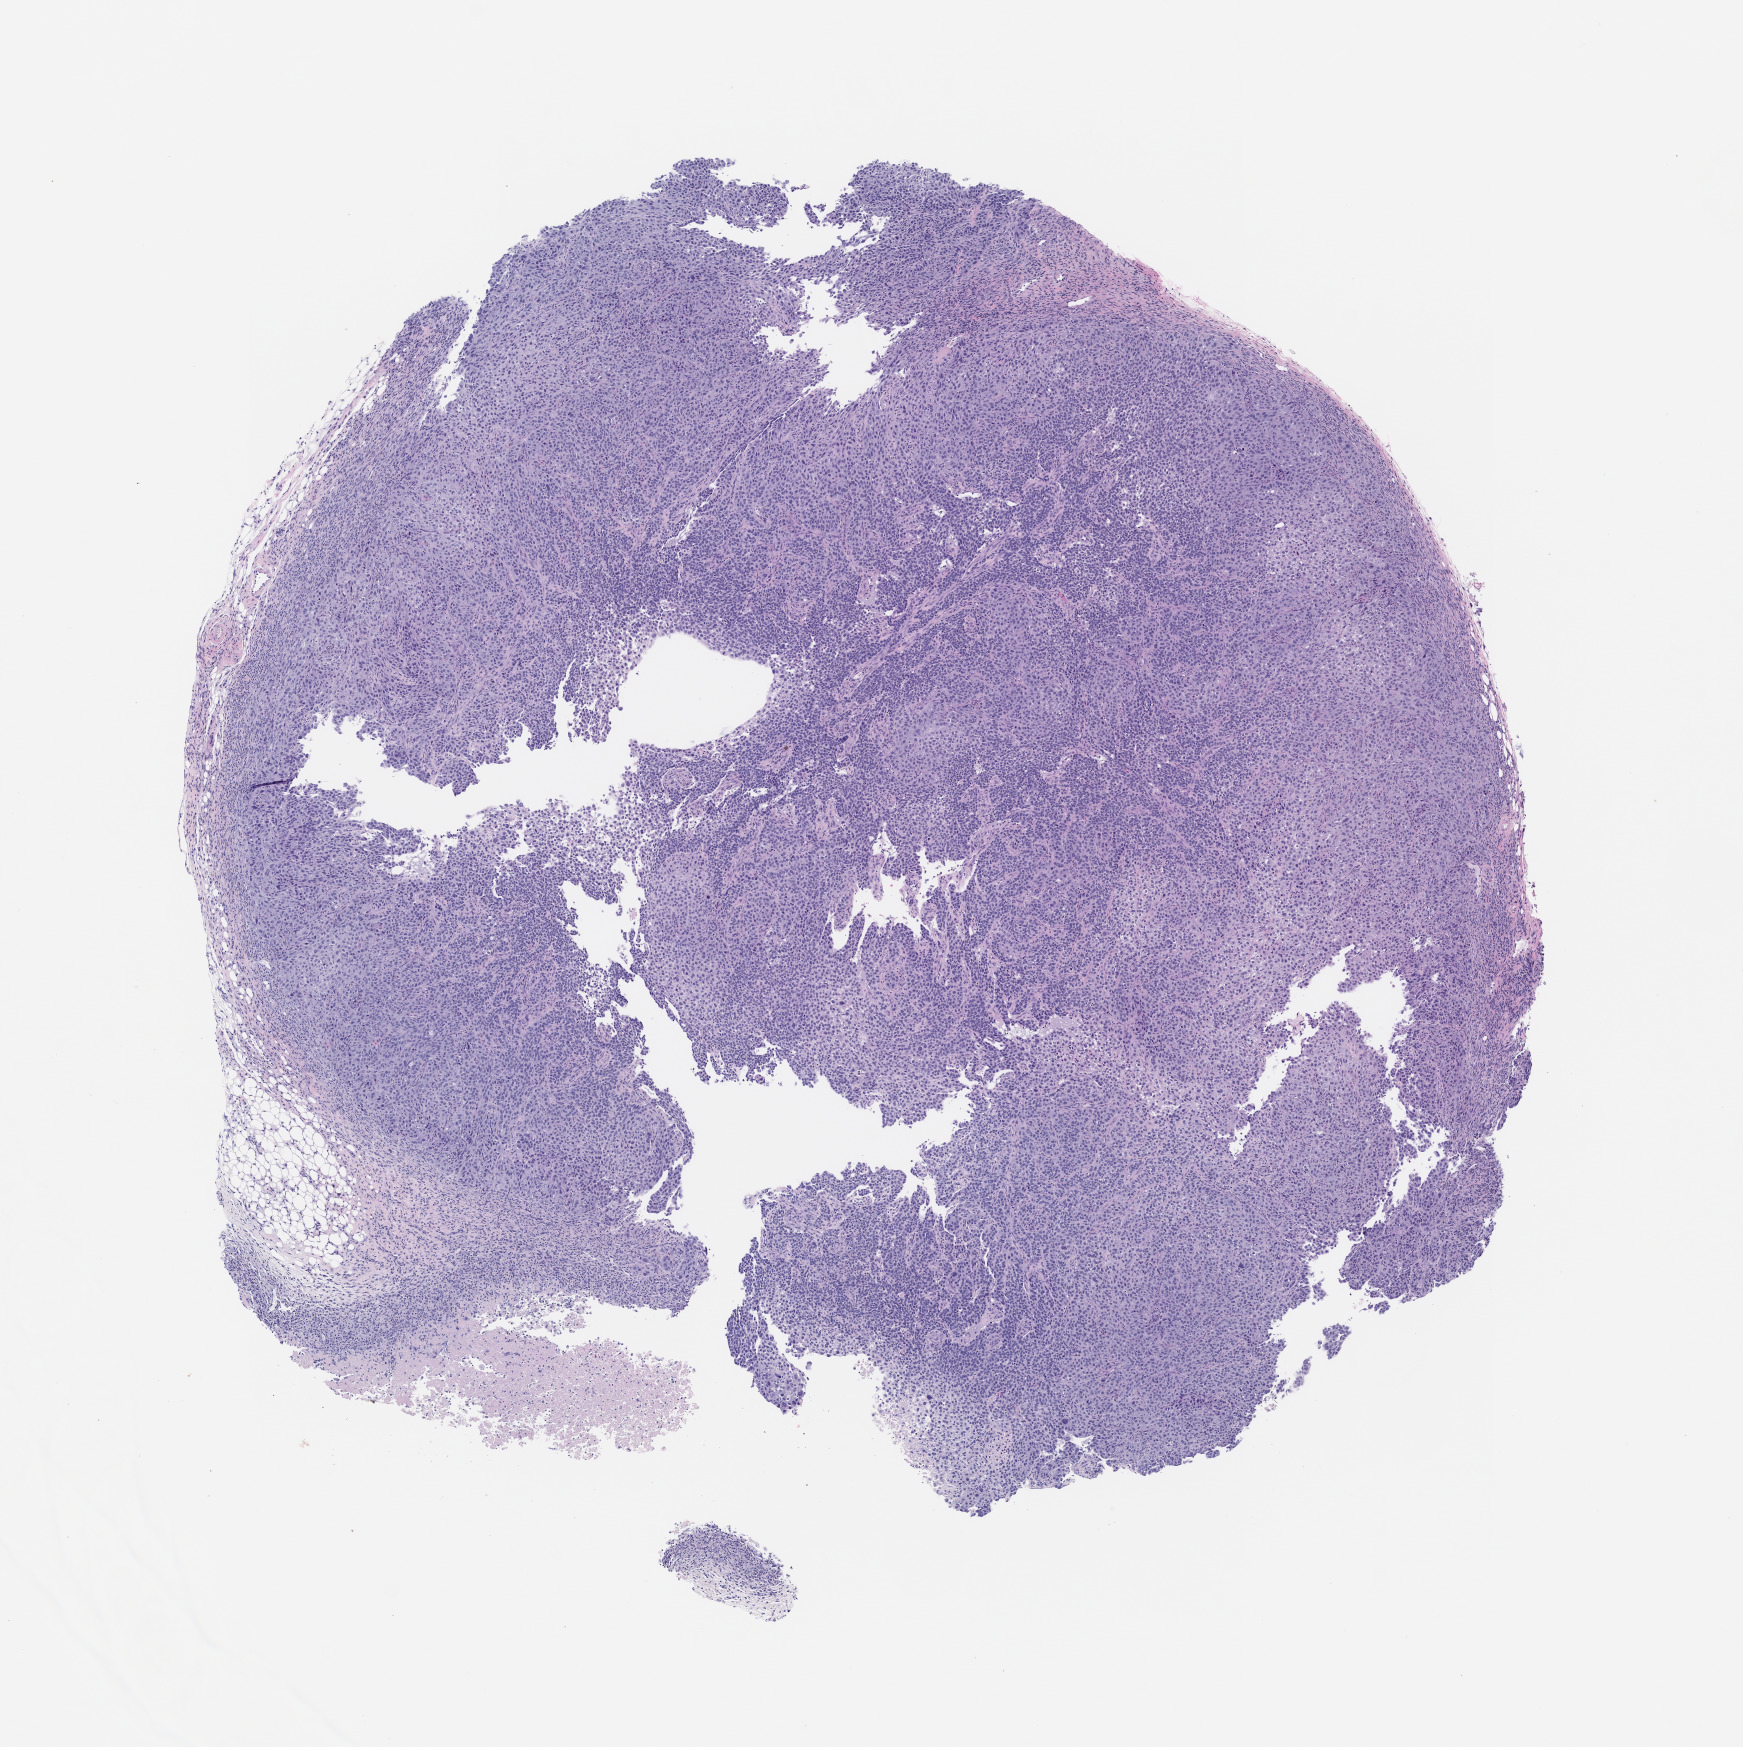
Hematoxylin and eosin (H&E) whole-slide image of a patient-derived xenograft (PDX) tumor grown in a mouse, passage 4, a low-resolution overview of the entire scanned area, about 7.0 x 7.0 mm. Formalin-fixed paraffin-embedded section. Tumor site category: bladder.
Originating patient diagnosis: Transitional Cell Carcinoma.